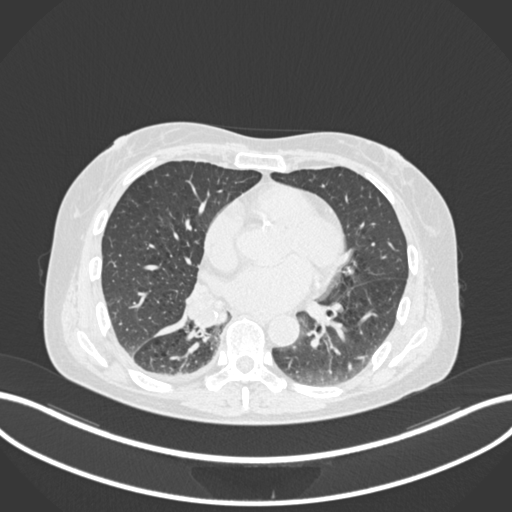
Chest CT, one axial slice; position 71 of 168 along the scan axis; 120 kVp; lung window (W 1500 / L -600 HU); 1 mm slice thickness; 512 × 512 image matrix. Female patient, age 63 years. From the clinical record (not read from this slice): clinical TNM (as recorded): T1c N0 M0.
Annotated regions visible in this slice (rectangle marked by the reading radiologist):
- lung tumour (recorded histology: adenocarcinoma): box from (x=183, y=281) to (x=228, y=332) px